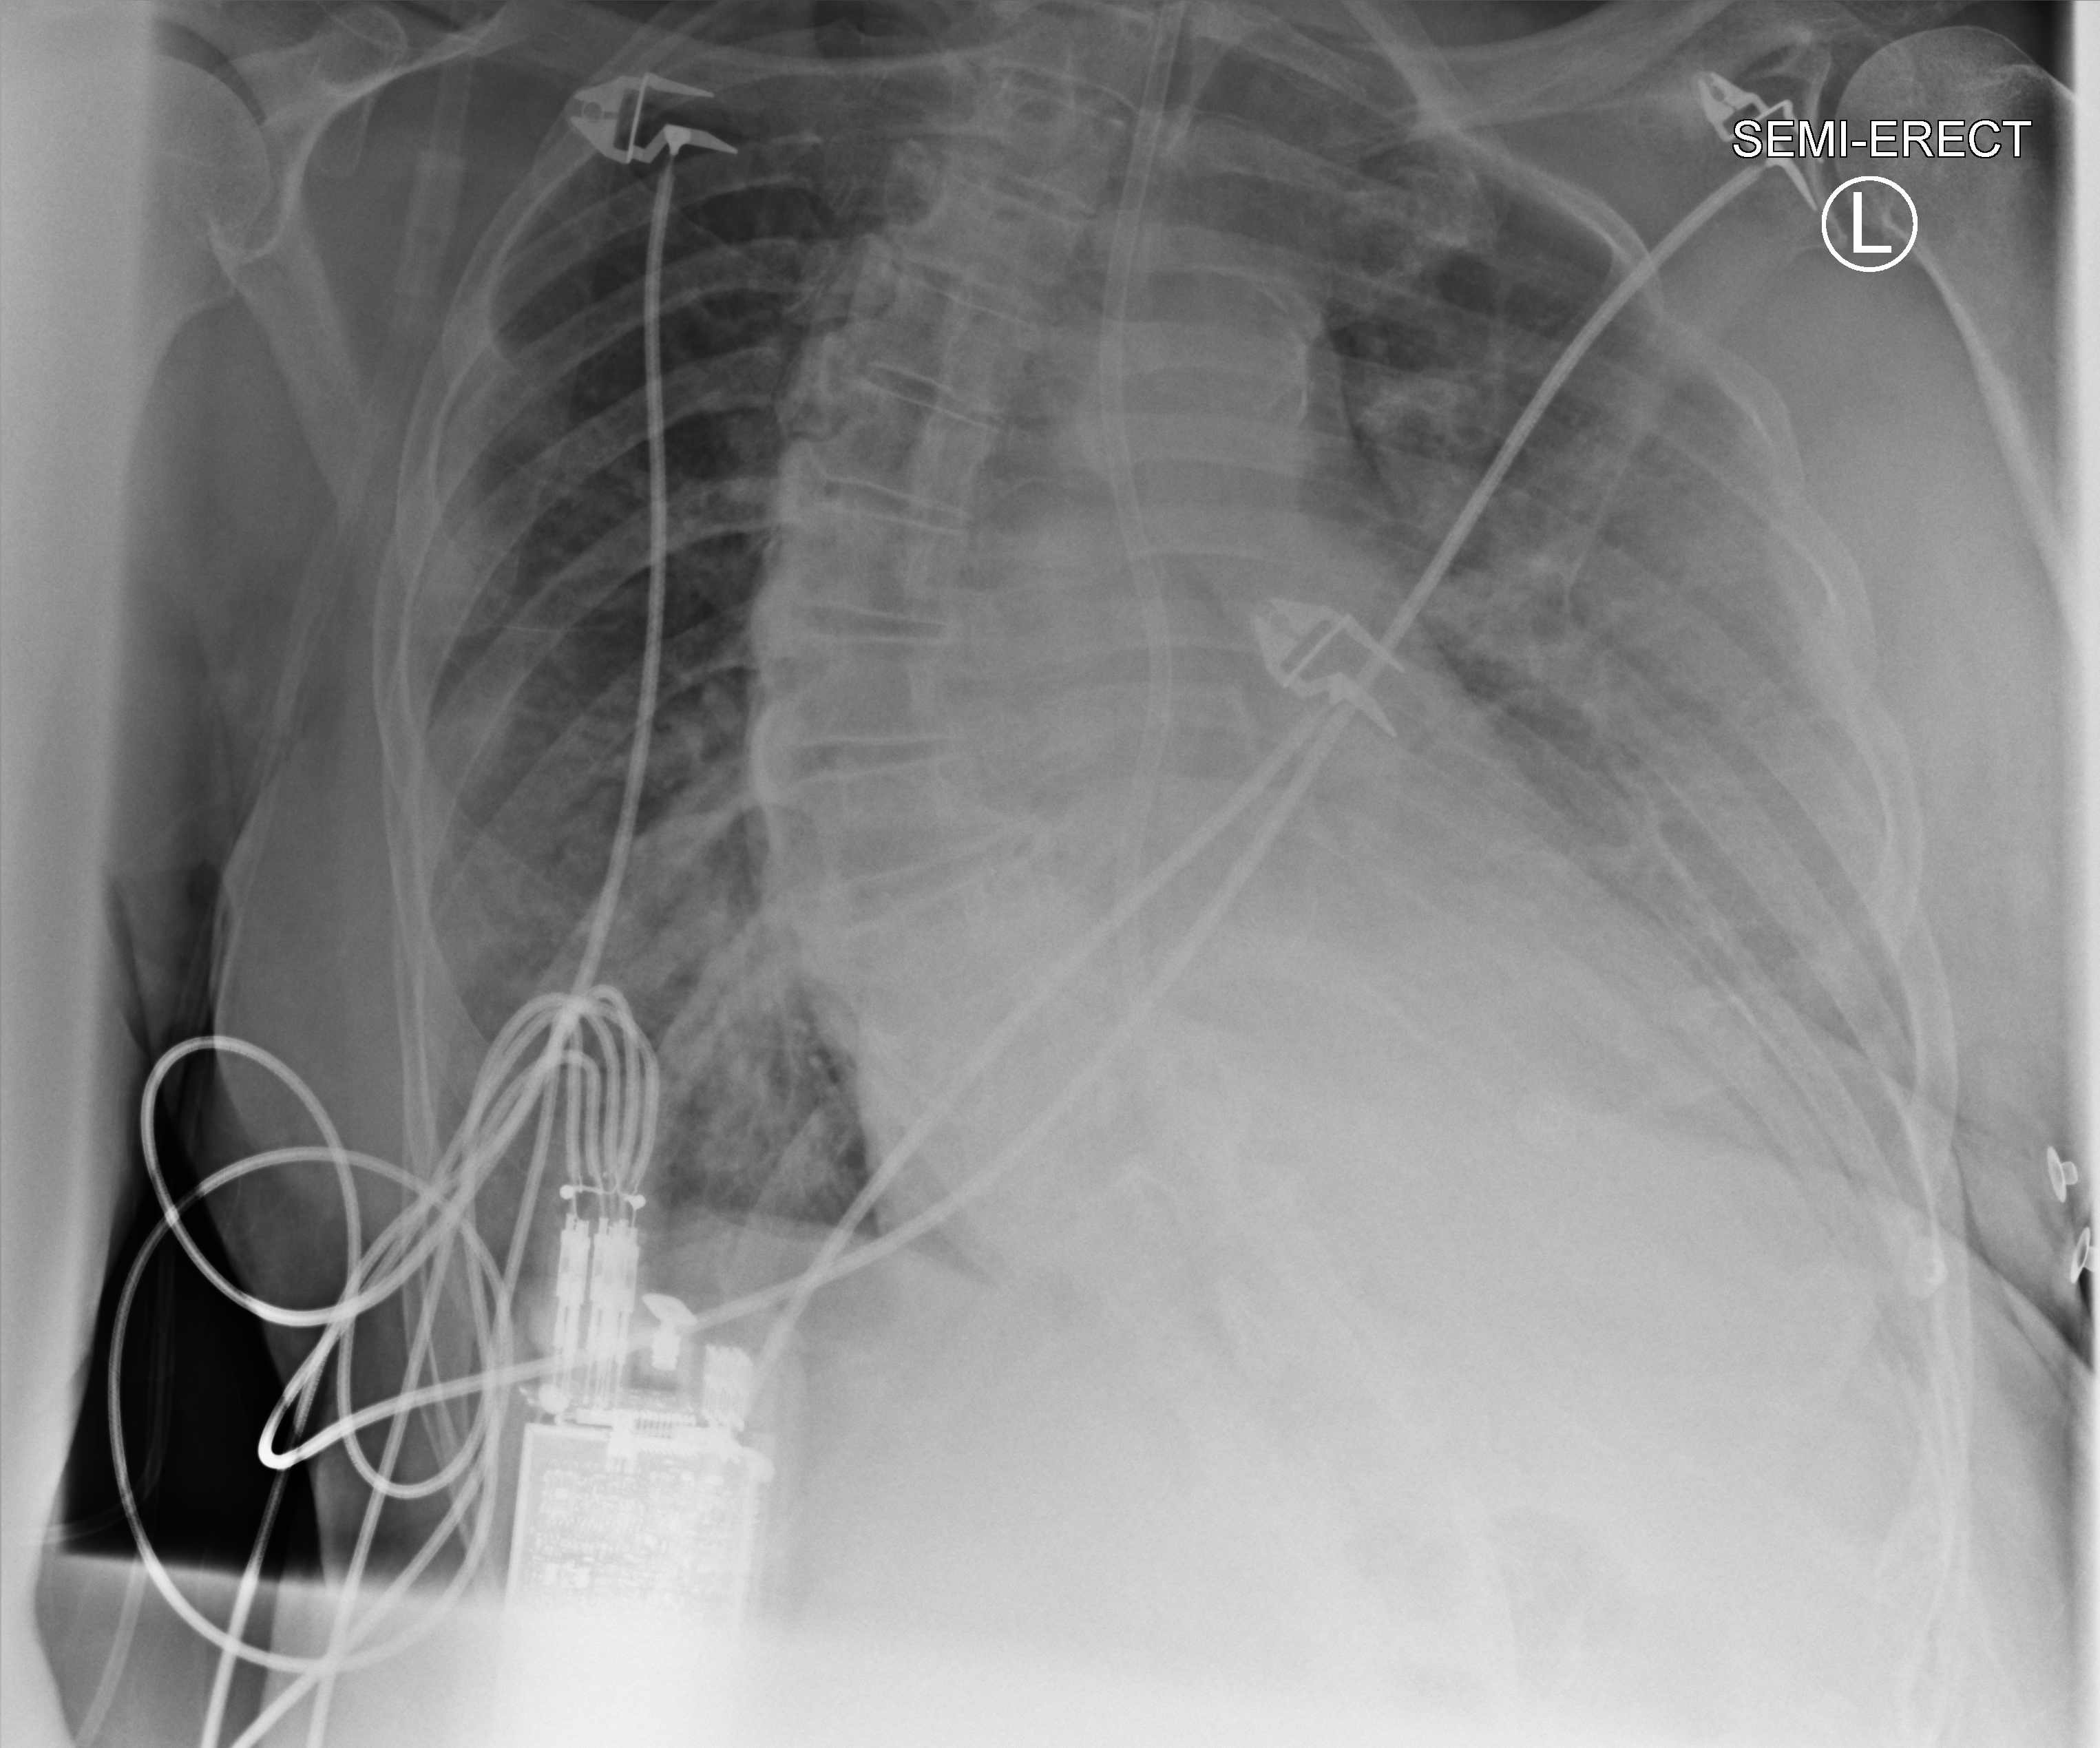
Bedside chest radiograph (computed radiography), anteroposterior (AP) projection. Male patient hospitalised with COVID-19, age 75–90 years.
From the hospital-stay record, not from the radiograph (when in the stay this image was taken is not recorded):
- admitted to intensive care during this hospital stay: no
- mechanically ventilated during this hospital stay: no